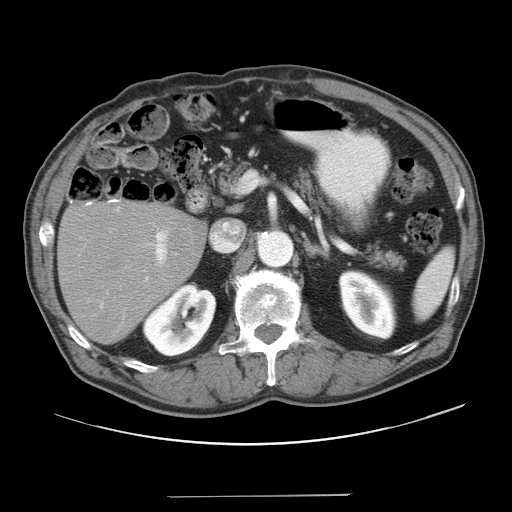
Contrast-enhanced abdominal CT, one axial slice. Reconstruction kernel STANDARD. 120 kVp. Intravenous contrast given. Soft-tissue window (W 400 / L 40 HU). 5 mm slice thickness. 512 × 512 image matrix, field of view 420 × 420 mm. Male patient, age 75 years. Case-level facts recorded for this patient, not image findings: diagnosis: colorectal cancer liver metastases, imaged before liver resection; multiple liver metastases: no; largest metastasis: 5.2 cm; chemotherapy before resection: no.
Annotated regions visible in this slice (manually delineated by an expert):
- liver: bounding box [x1, y1, x2, y2] px = [60, 203, 205, 344]
- planned liver remnant (the part of the liver to remain after resection): [60, 203, 205, 344]
- portal vein (with intrahepatic branches): [99, 206, 169, 309]